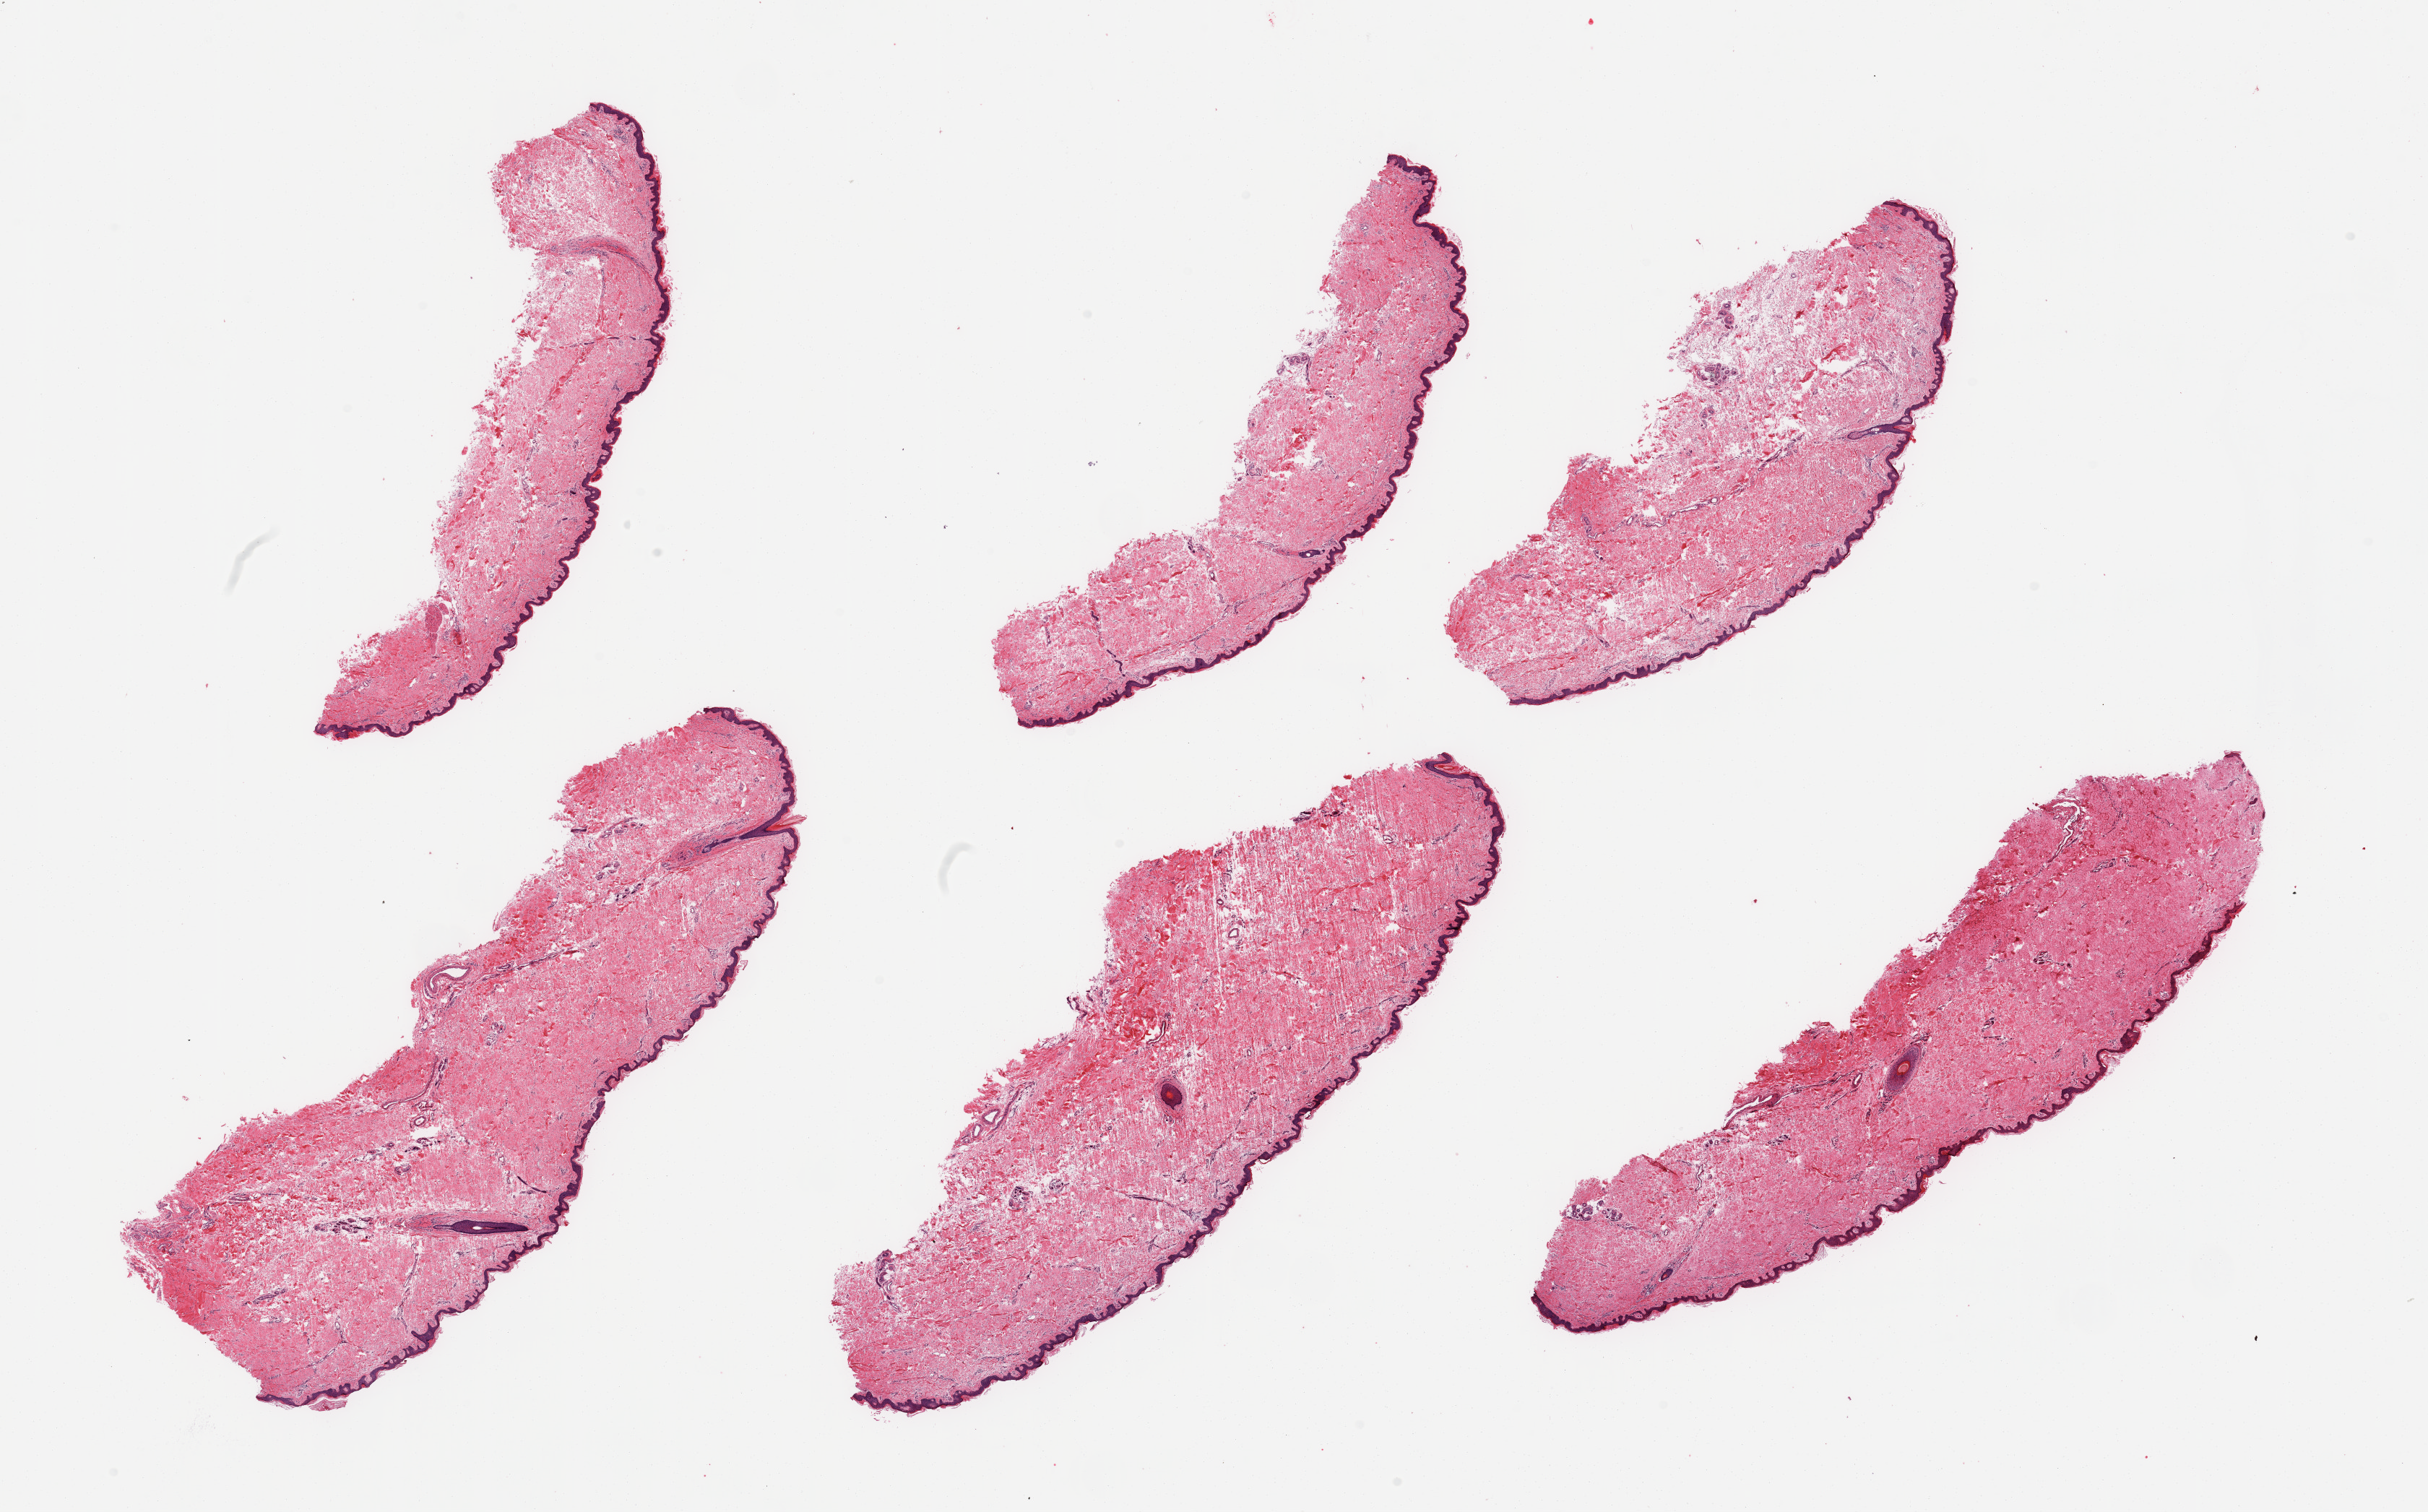
Hematoxylin and eosin (H&E) whole-slide image, low-resolution overview of the scanned area, about 26.6 x 16.6 mm (from a 20x scan); PAXgene-fixed, paraffin-embedded tissue; target tissue: skin of lower leg; donor tissue sample. Male donor.
Pathologist's review note for this sample: 6 pieces, no significant dermal fat; squamous epithelium up to ~40-50 microns.